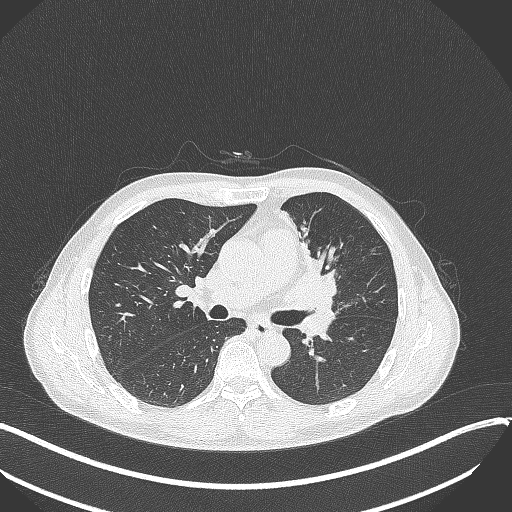
Chest CT, one axial slice; position 193 of 411 along the scan axis; lung window (W 1500 / L -600 HU); 1 mm slice thickness; 512 × 512 image matrix, field of view 400 × 400 mm. Male patient, age 56 years. Case-level facts recorded for this patient, not image findings: clinical TNM (as recorded): T2a N0 M0.
Structures marked on this image (rectangle marked by the reading radiologist):
- lung tumour (recorded histology: squamous cell carcinoma): bounding box (x1, y1, x2, y2) in pixels: (278, 254, 348, 312)